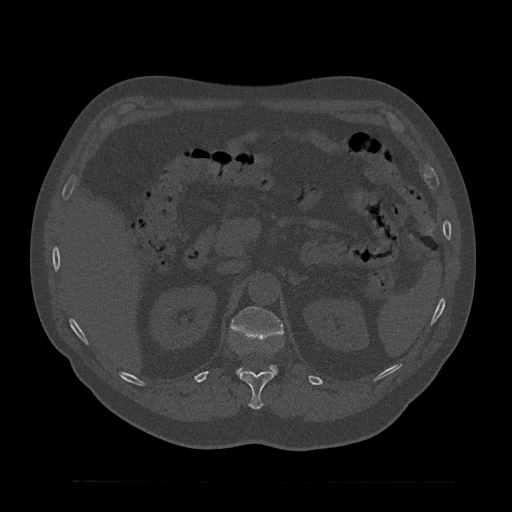
CT including the spine, one axial slice; slice 203 of 797 in the series (ordered by position); reconstruction kernel Br40s/3; bone window (W 1800 / L 400 HU); 0.5 mm slice thickness; 512 × 512 image matrix. Male patient, age 61 years. From the clinical record (not read from this slice): primary cancer: prostate.
Structures marked on this image (semi-automatic segmentation, software-assisted and operator-edited):
- L1 vertebra: bounding box (x1, y1, x2, y2) in pixels: (231, 306, 283, 375)
- T12 vertebra: (239, 371, 274, 410)